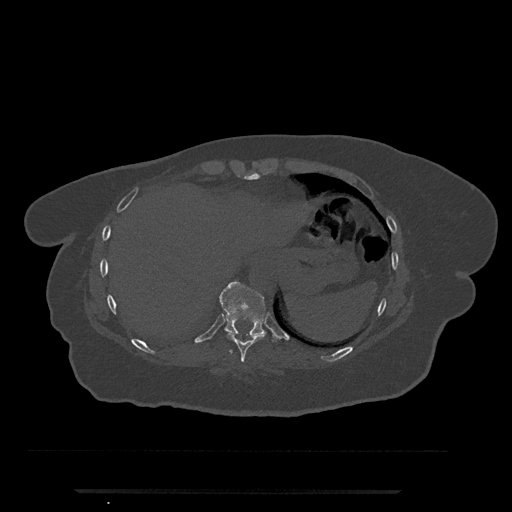
CT including the spine, one axial slice. Slice 313 of 797 in the series (ordered by position). Reconstruction kernel Br40s/3. 120 kVp. Bone window (W 1800 / L 400 HU). 512 × 512 image matrix. Patient: female, 51 years. Case-level facts recorded for this patient, not image findings: primary cancer: neuro; vertebrae with lytic lesions (as recorded): T8.
Structures marked on this image (semi-automatically segmented with operator editing):
- T10 vertebra: bounding box <219,281,267,338> (left, top, right, bottom; pixels)
- T9 vertebra: <227,333,266,362>